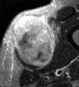
MRI of an extremity soft-tissue mass, one axial slice; slice 20 of 45 in the series (ordered by position); STIR; MR volume resampled by the dataset authors to the PET/CT grid (not the native acquisition matrix); 3.27 mm slice thickness; 79 × 87 image matrix, field of view 77 × 85 mm. Male patient. Case-level facts recorded for this patient, not image findings: histological type: pleiomorphic leiomyosarcoma; grade: high; site of the primary tumour: left thigh.
Outlined on this slice (expert contour drawn on MRI and transferred to this co-registered scan by the dataset authors):
- gross tumour volume including surrounding oedema: bounding box [x1, y1, x2, y2] px = [11, 14, 60, 67]
- gross tumour volume (mass): [11, 16, 55, 67]